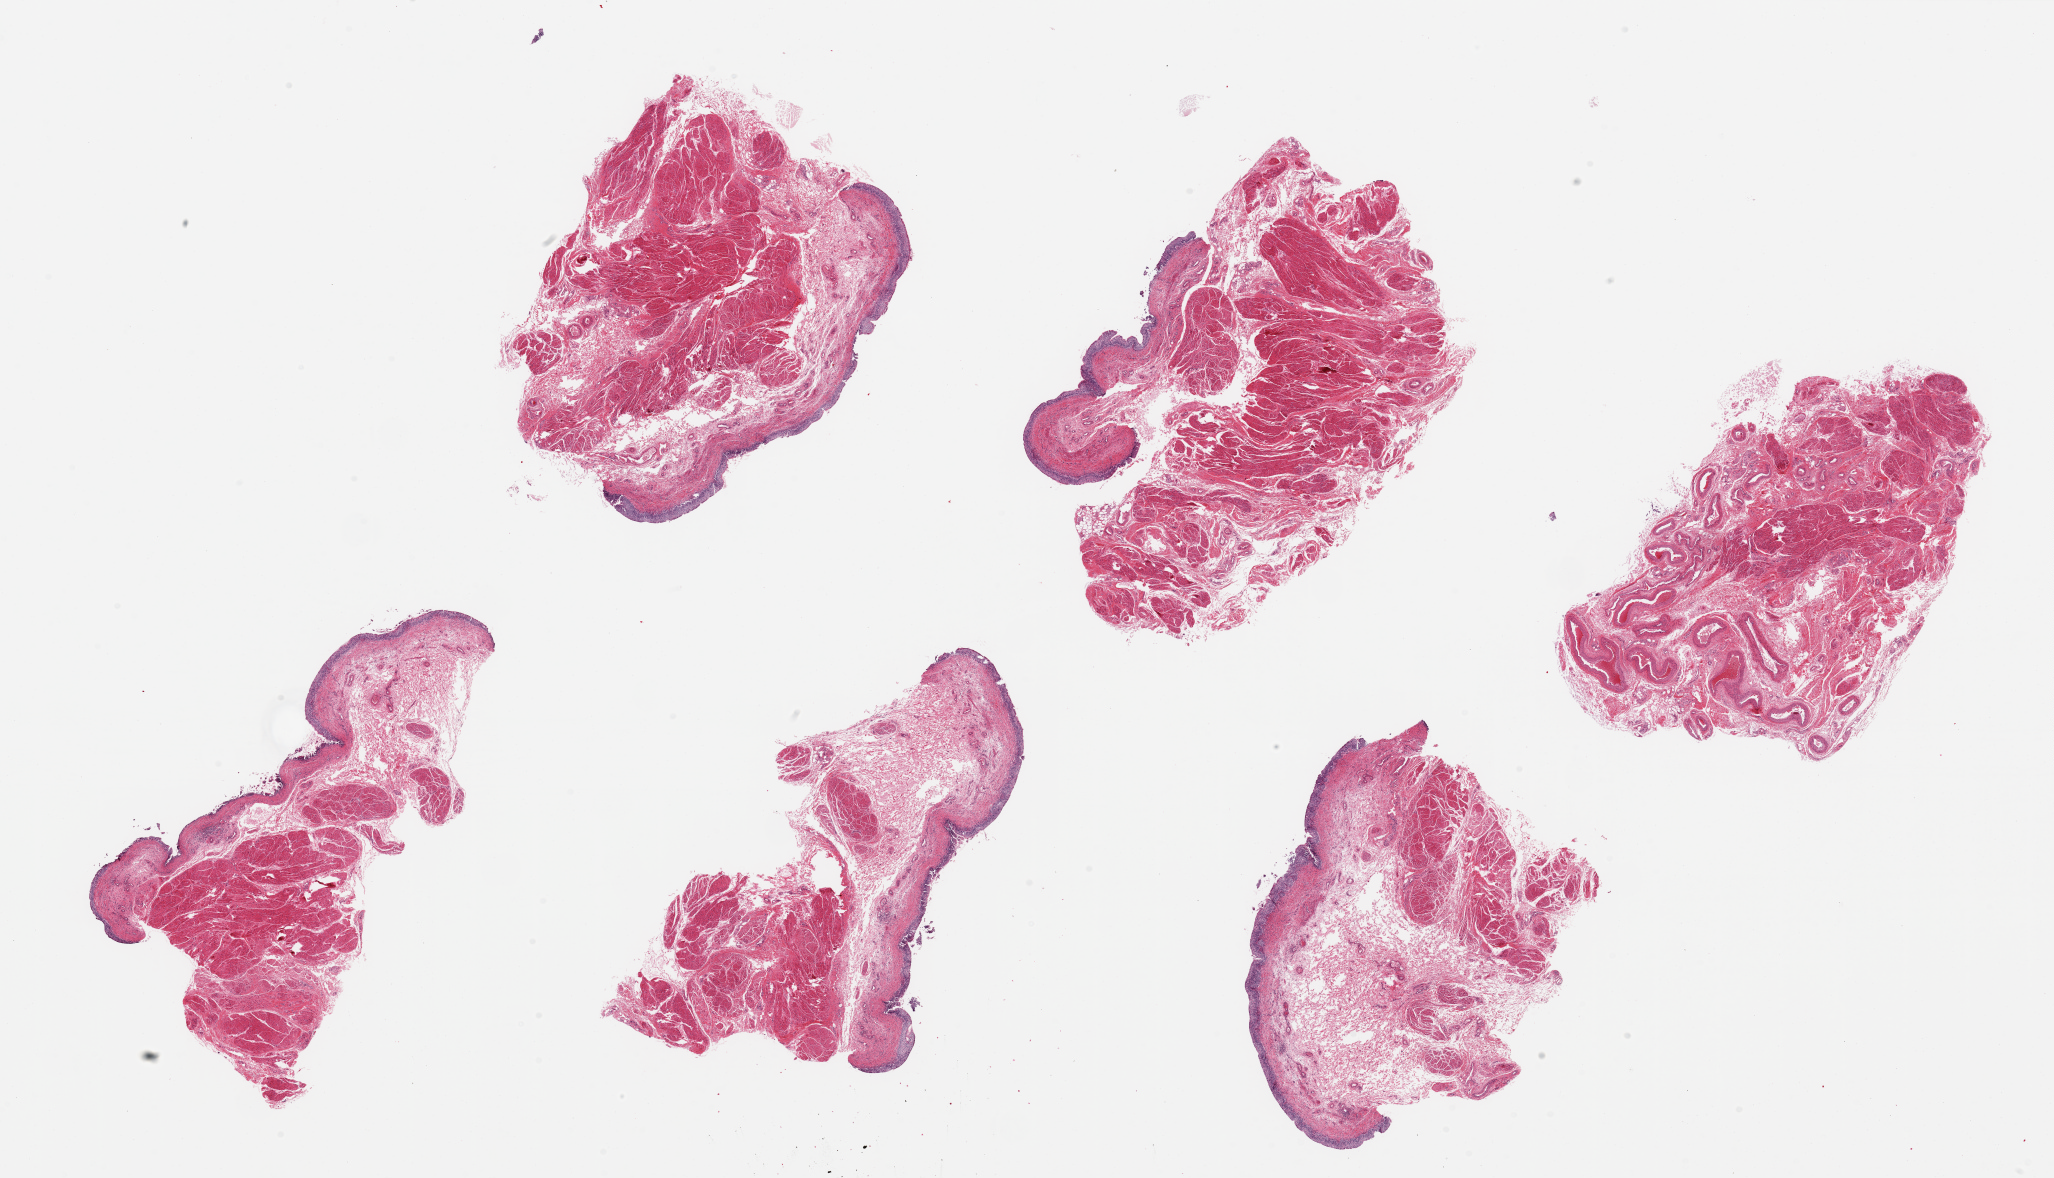
Digitized haematoxylin and eosin-stained section — shown as a low-resolution overview of the whole scanned area (about 32.5 x 18.6 mm, acquisition: 20x scan). PAXgene-fixed, paraffin-embedded tissue. Section of urinary bladder (target tissue). Tissue donor sample.
Pathologist's review note for this sample: 6 pieces, ~6x4 mm; urothelium unusually well-preserved, ~5% of thickness.